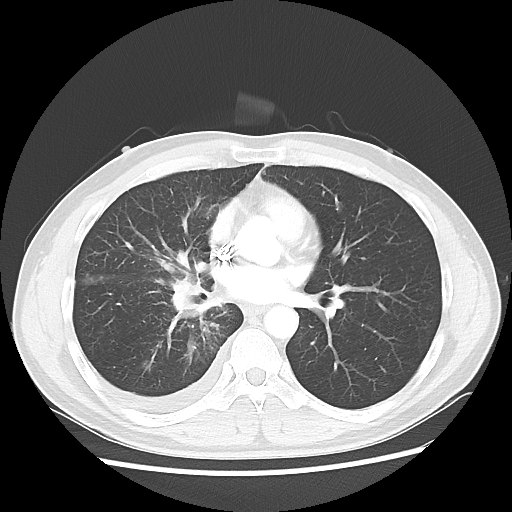
Chest CT, one axial slice; reconstruction kernel LUNG; lung window (W 1500 / L -600 HU); 5 mm slice thickness; 512 × 512 image matrix, field of view 360 × 360 mm. Patient: male, 46 years. From the clinical record (not read from this slice): clinical TNM (as recorded): T2 N3 M1.
Structures marked on this image (bounding box drawn by a radiologist):
- lung tumour (recorded histology: adenocarcinoma): bounding box (x1, y1, x2, y2) in pixels: (164, 277, 207, 330)